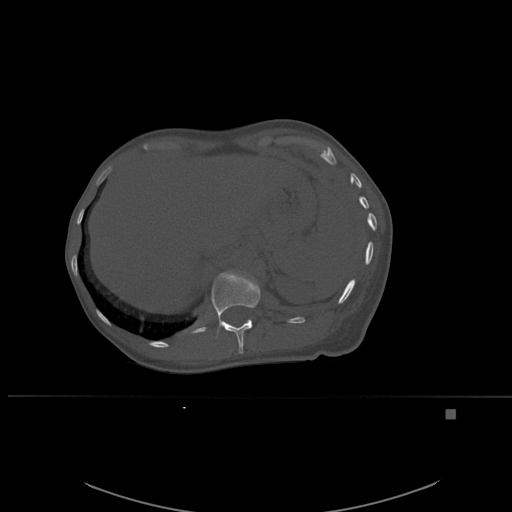
CT including the spine, one axial slice; slice 277 of 537 in the series (ordered by position); bone window (W 1800 / L 400 HU); 1.5 mm slice thickness; 512 × 512 image matrix, field of view 440 × 440 mm. Patient: female, 45 years. From the clinical record (not read from this slice): primary cancer: lung.
Outlined on this slice (semi-automatic segmentation, software-assisted and operator-edited):
- T12 vertebra: bounding box <211,271,261,354> (left, top, right, bottom; pixels)